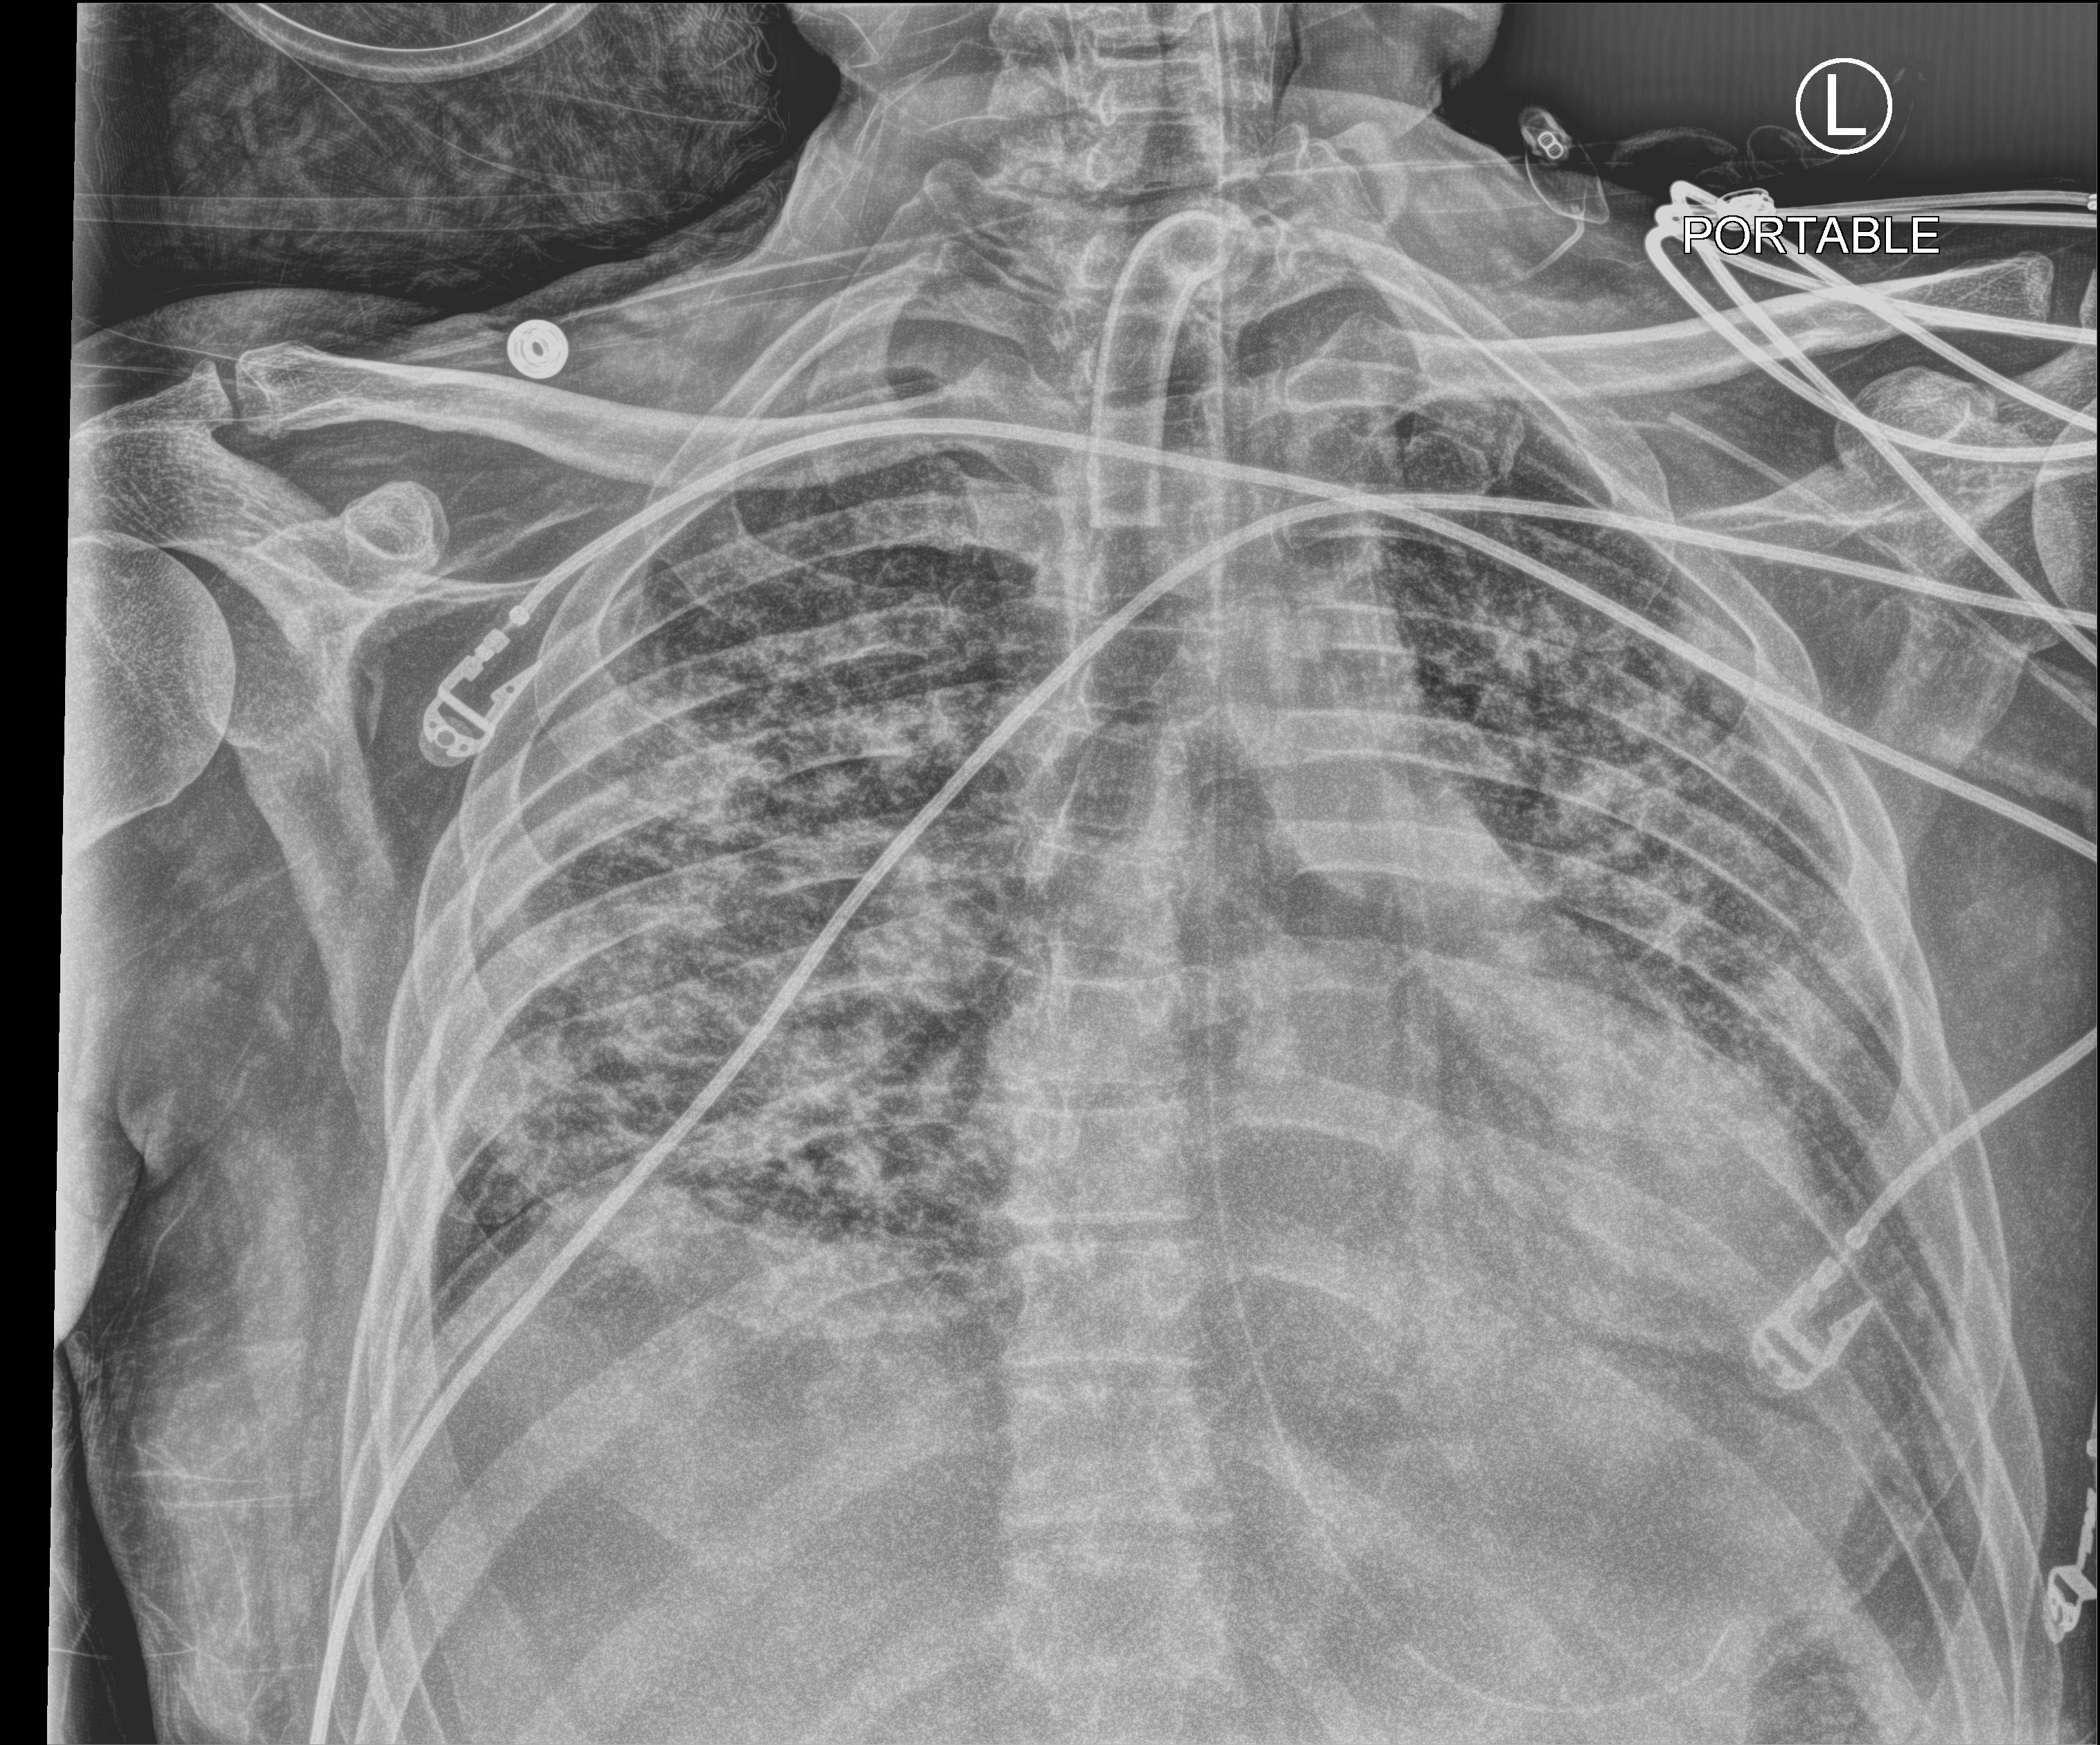
Chest X-ray (portable); anteroposterior (AP) projection. Patient hospitalised with COVID-19; male, aged 18–59 years.
From the hospital-stay record, not from the radiograph (when in the stay this image was taken is not recorded): admitted to intensive care during this hospital stay: yes; mechanically ventilated during this hospital stay: yes.